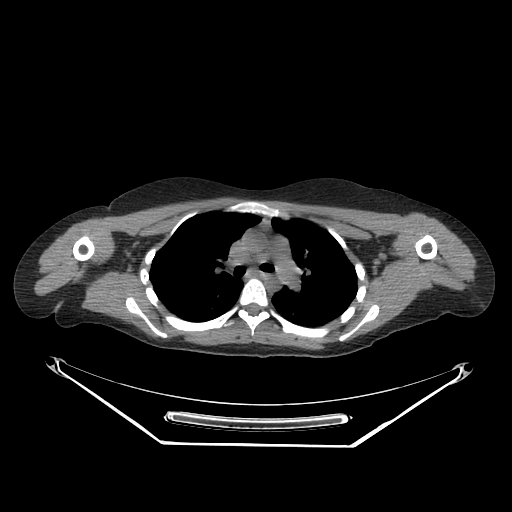
CT of an extremity soft-tissue mass (from a PET/CT study), one axial slice. Slice 199 of 267 in the series (ordered by position). Reconstruction kernel SOFT. 140 kVp. Soft-tissue window (W 400 / L 40 HU). 3.75 mm slice thickness. 512 × 512 image matrix, field of view 500 × 500 mm. Female patient. Case-level facts recorded for this patient, not image findings: histological type: malignant fibrous histiocytoma; grade: low; site of the primary tumour: left arm.
Annotated regions visible in this slice (expert contour drawn on MRI and transferred to this co-registered scan by the dataset authors):
- gross tumour volume (mass): box from (x=438, y=260) to (x=457, y=277) px